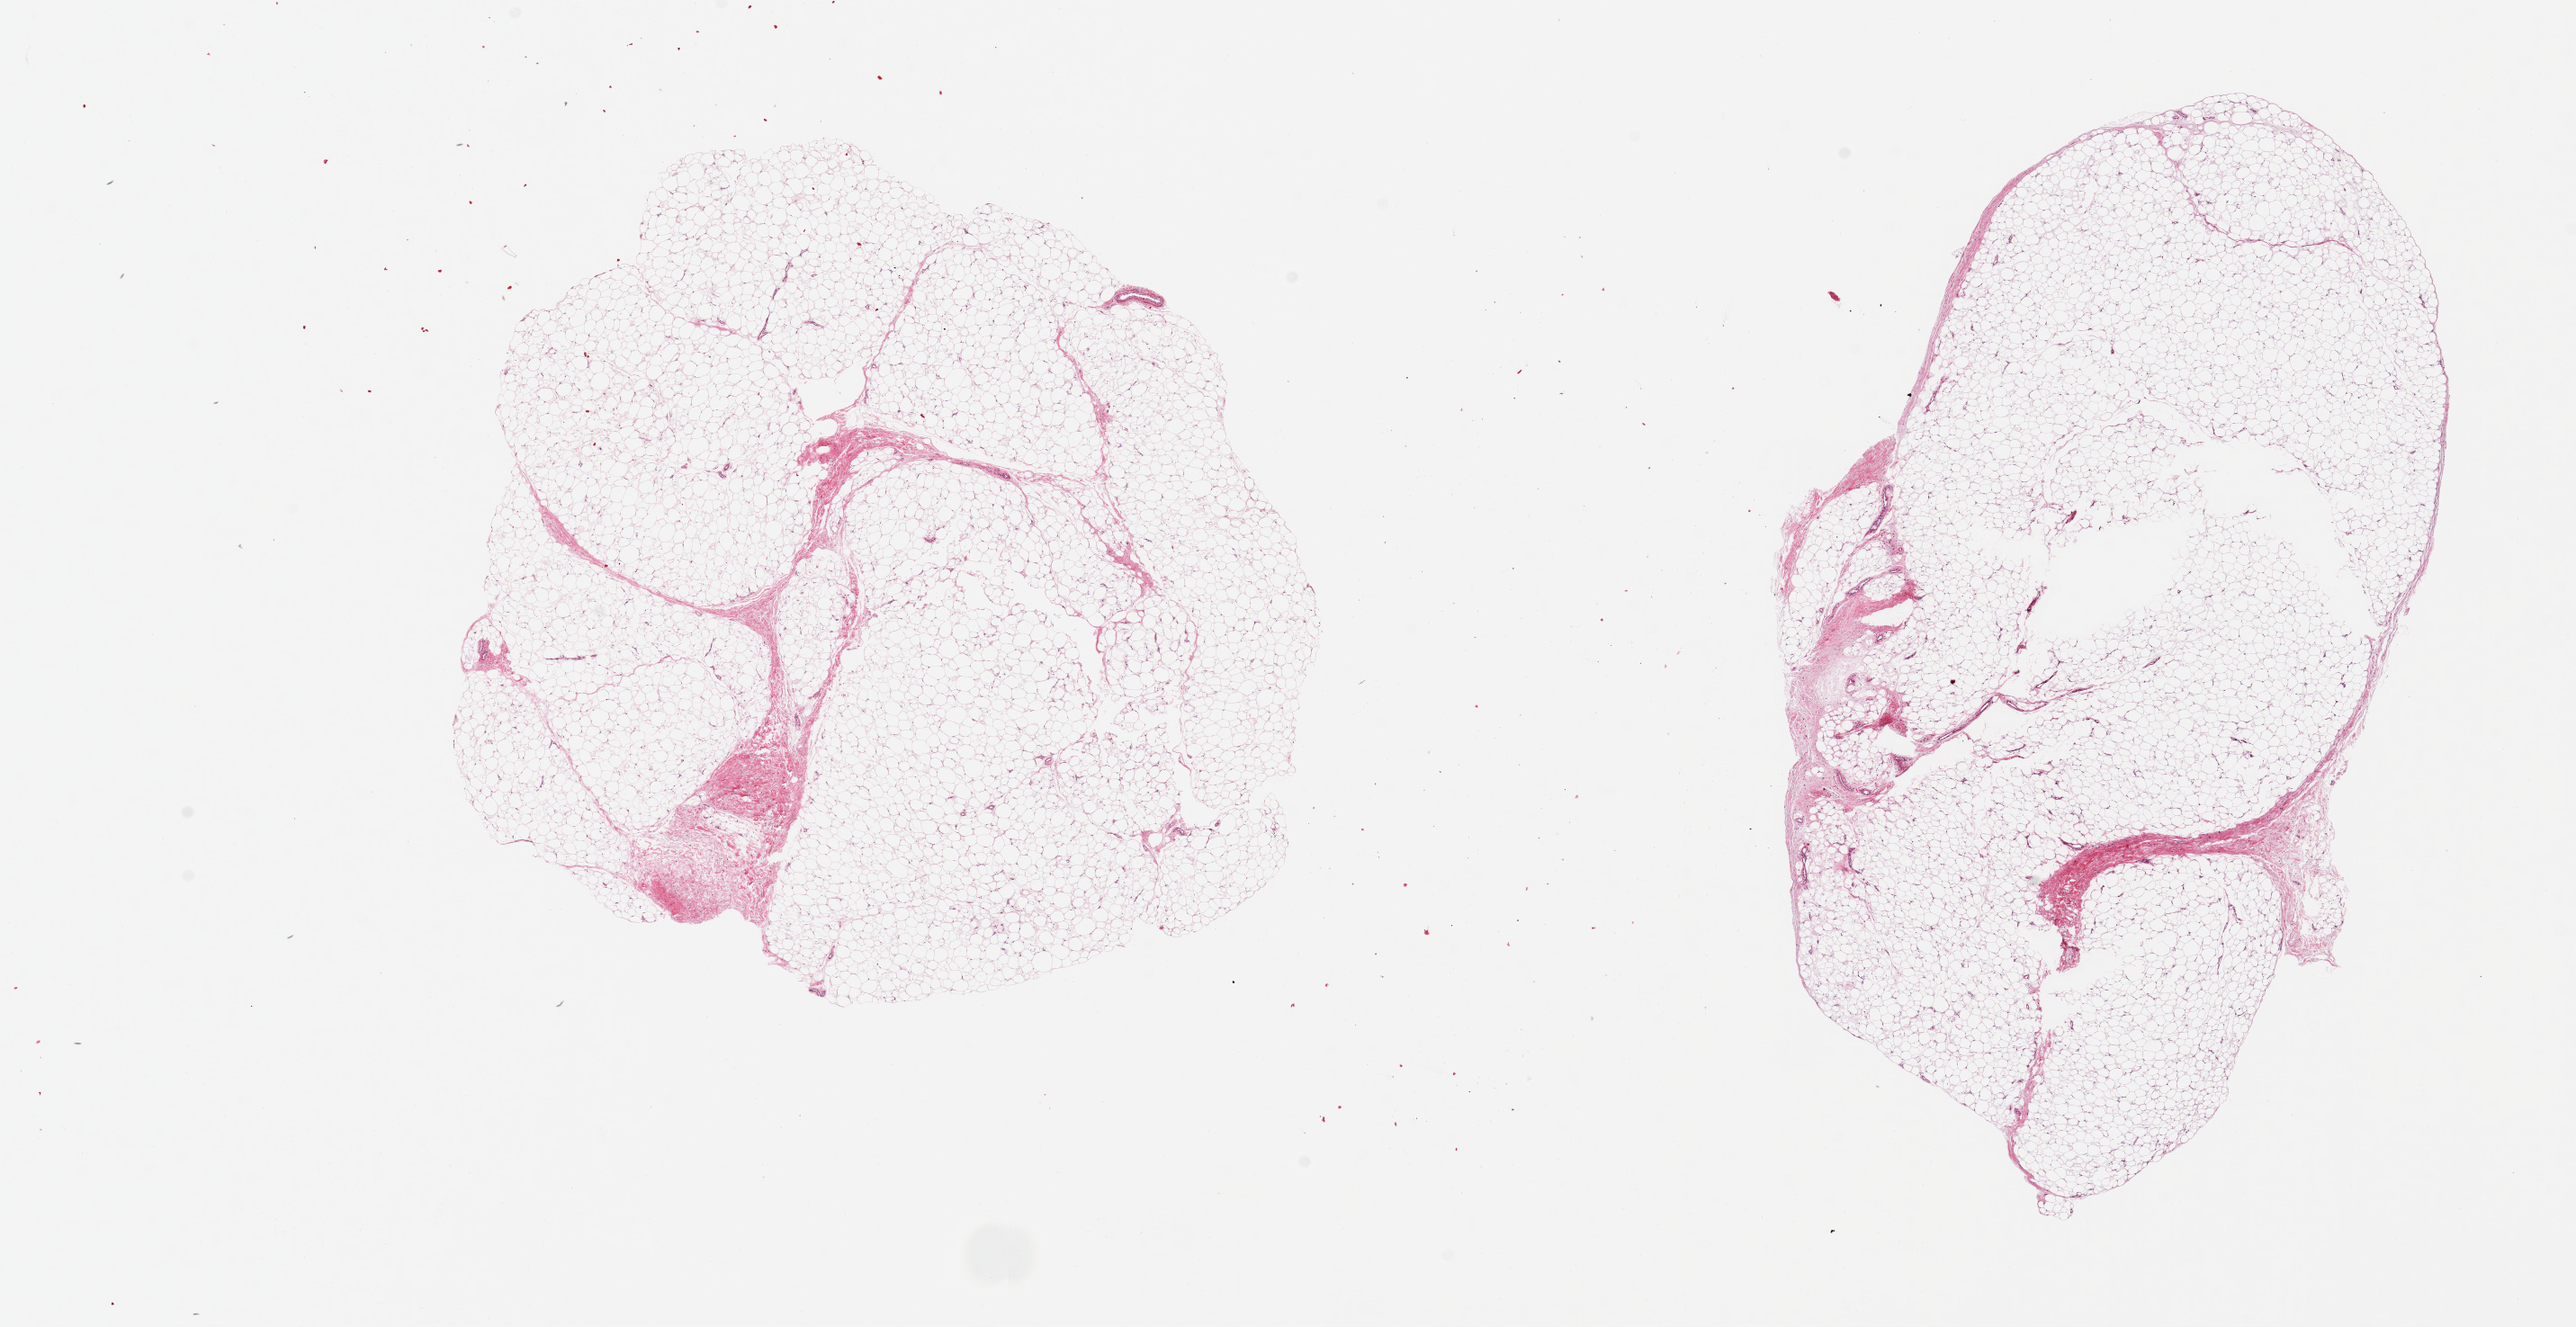
Digitized hematoxylin and eosin (H&E)-stained section, shown as a low-resolution overview of the whole scanned area (about 22.6 x 11.7 mm), PAXgene-fixed paraffin-embedded (PFPE) section, target tissue: adipose tissue, donor tissue sample.
Reviewer comment on this tissue sample: 2 pieces, 8x7 & 10x5.5mm; 10% central hole in one piece.